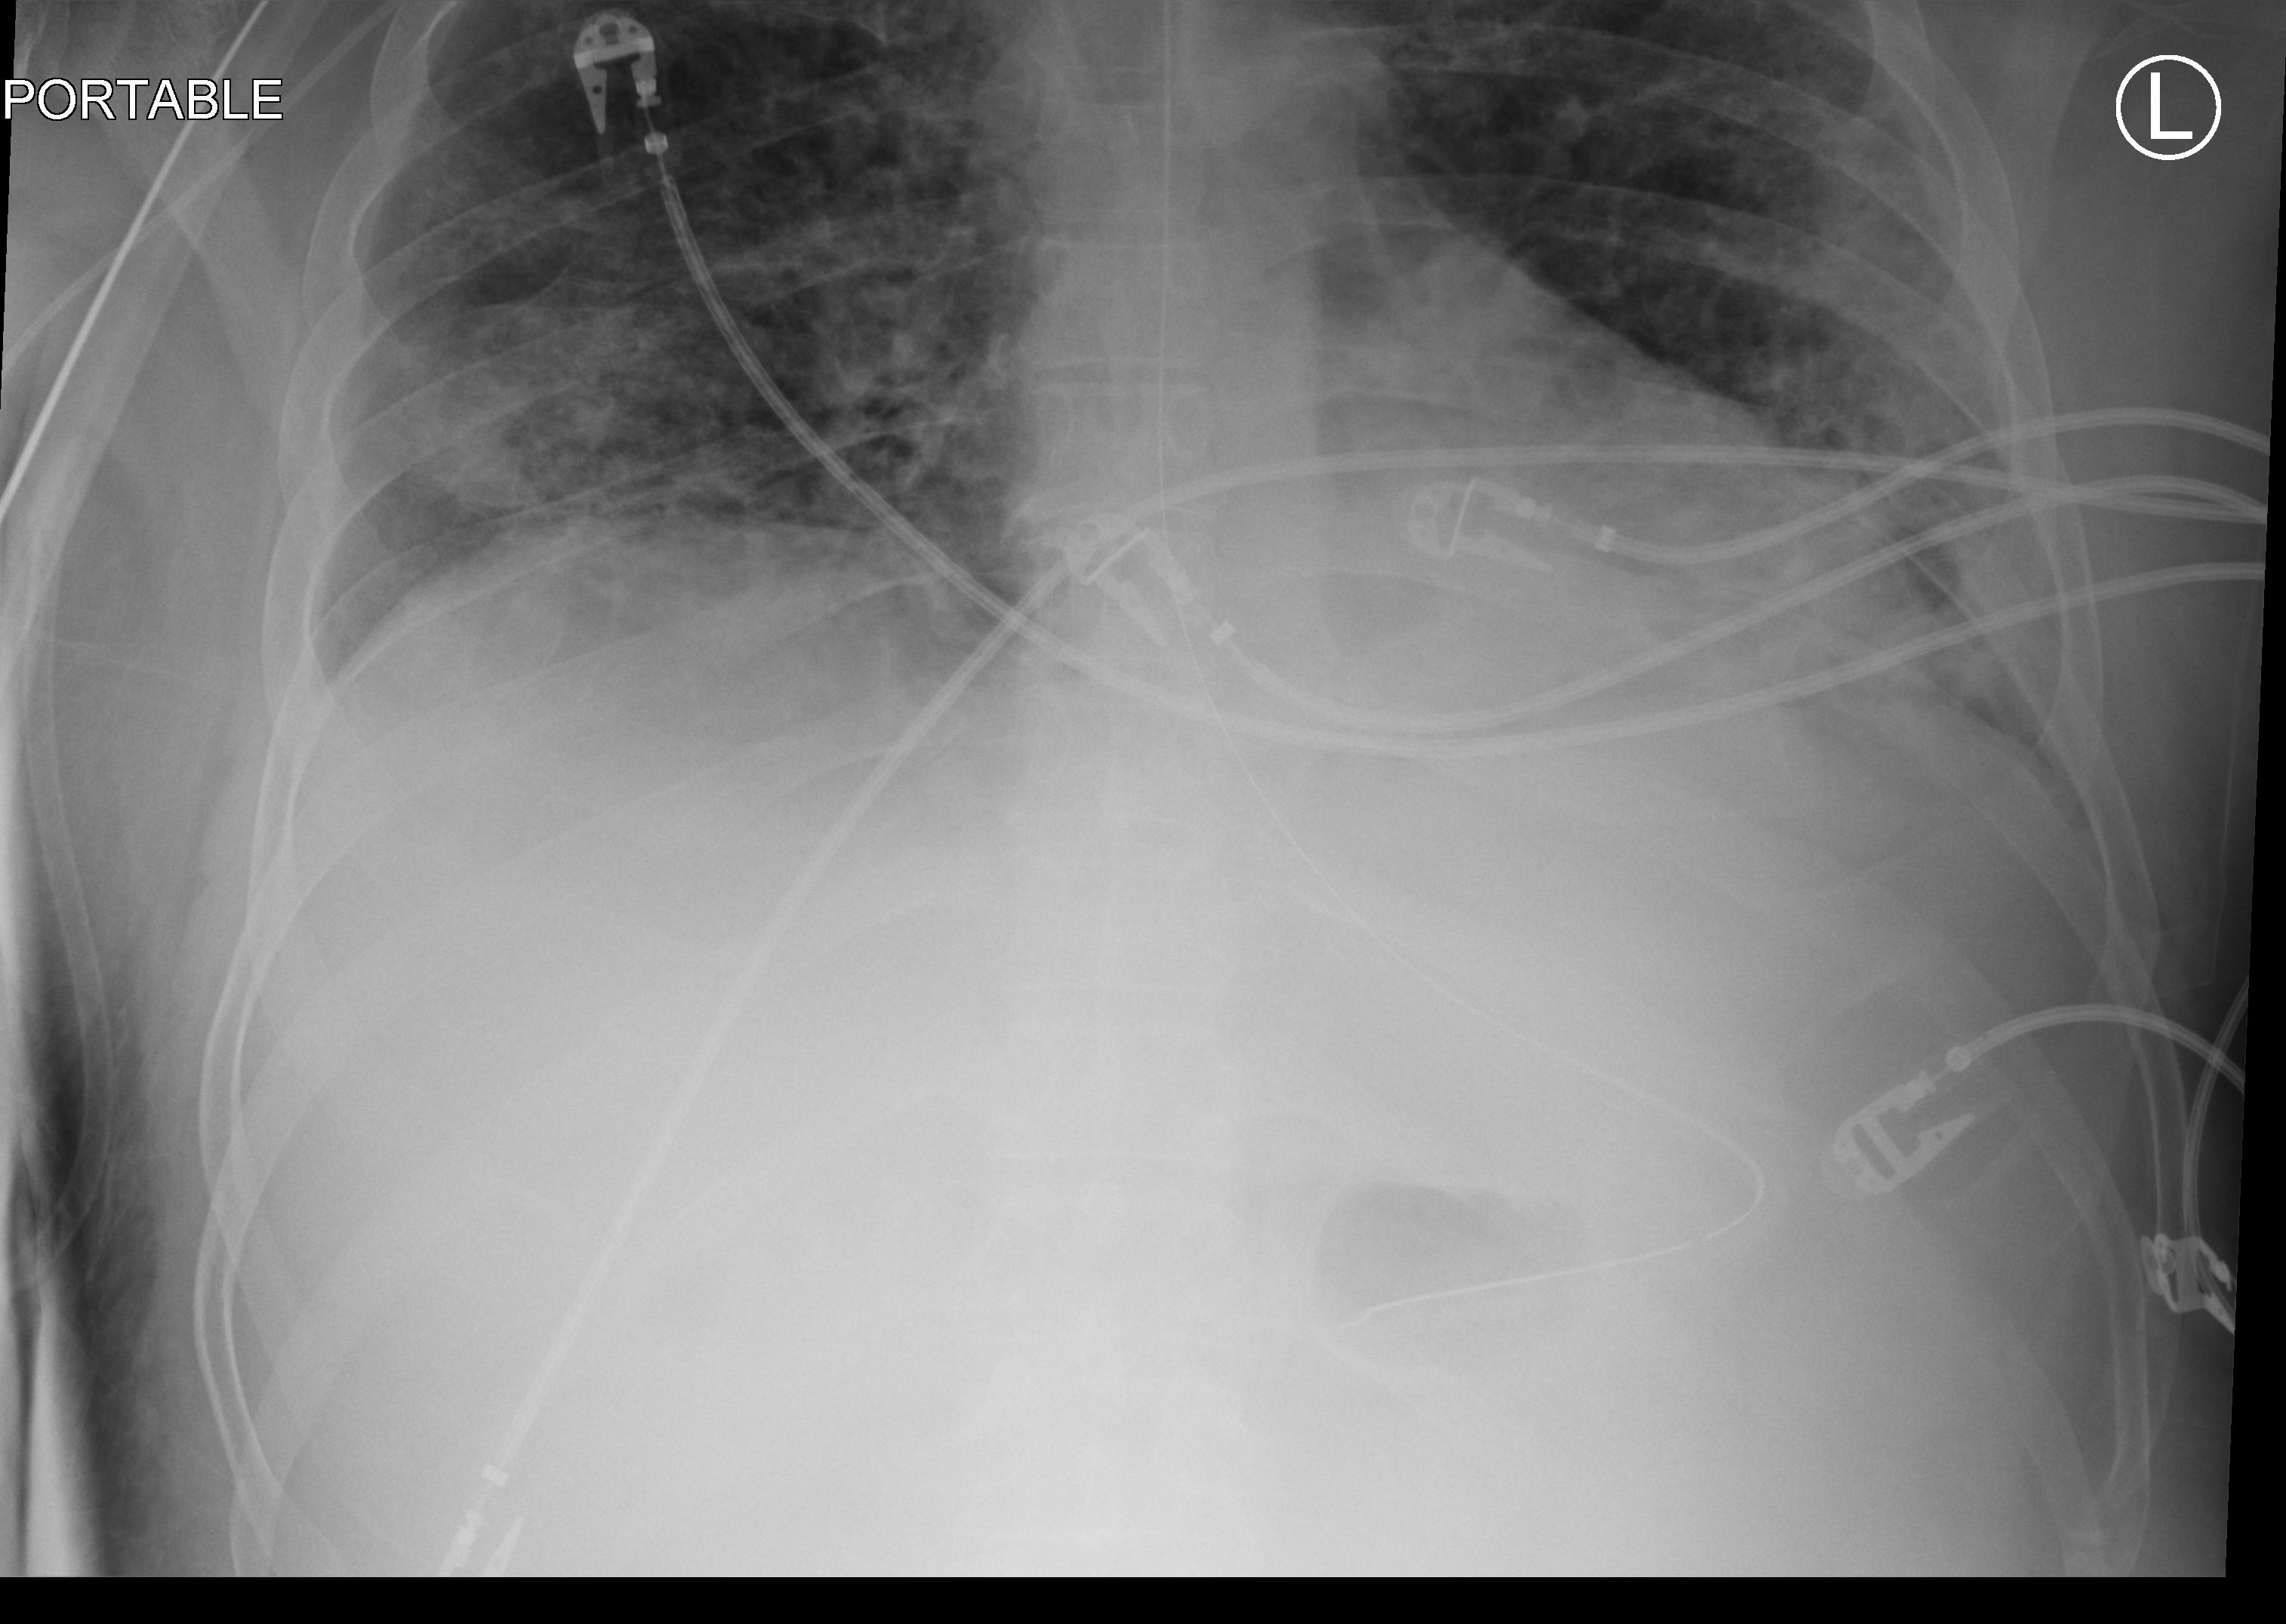
Chest X-ray (portable); anteroposterior (AP) projection. Male patient hospitalised with COVID-19, age 18–59 years.
From the hospital-stay record, not from the radiograph (when in the stay this image was taken is not recorded): admitted to intensive care during this hospital stay: yes.